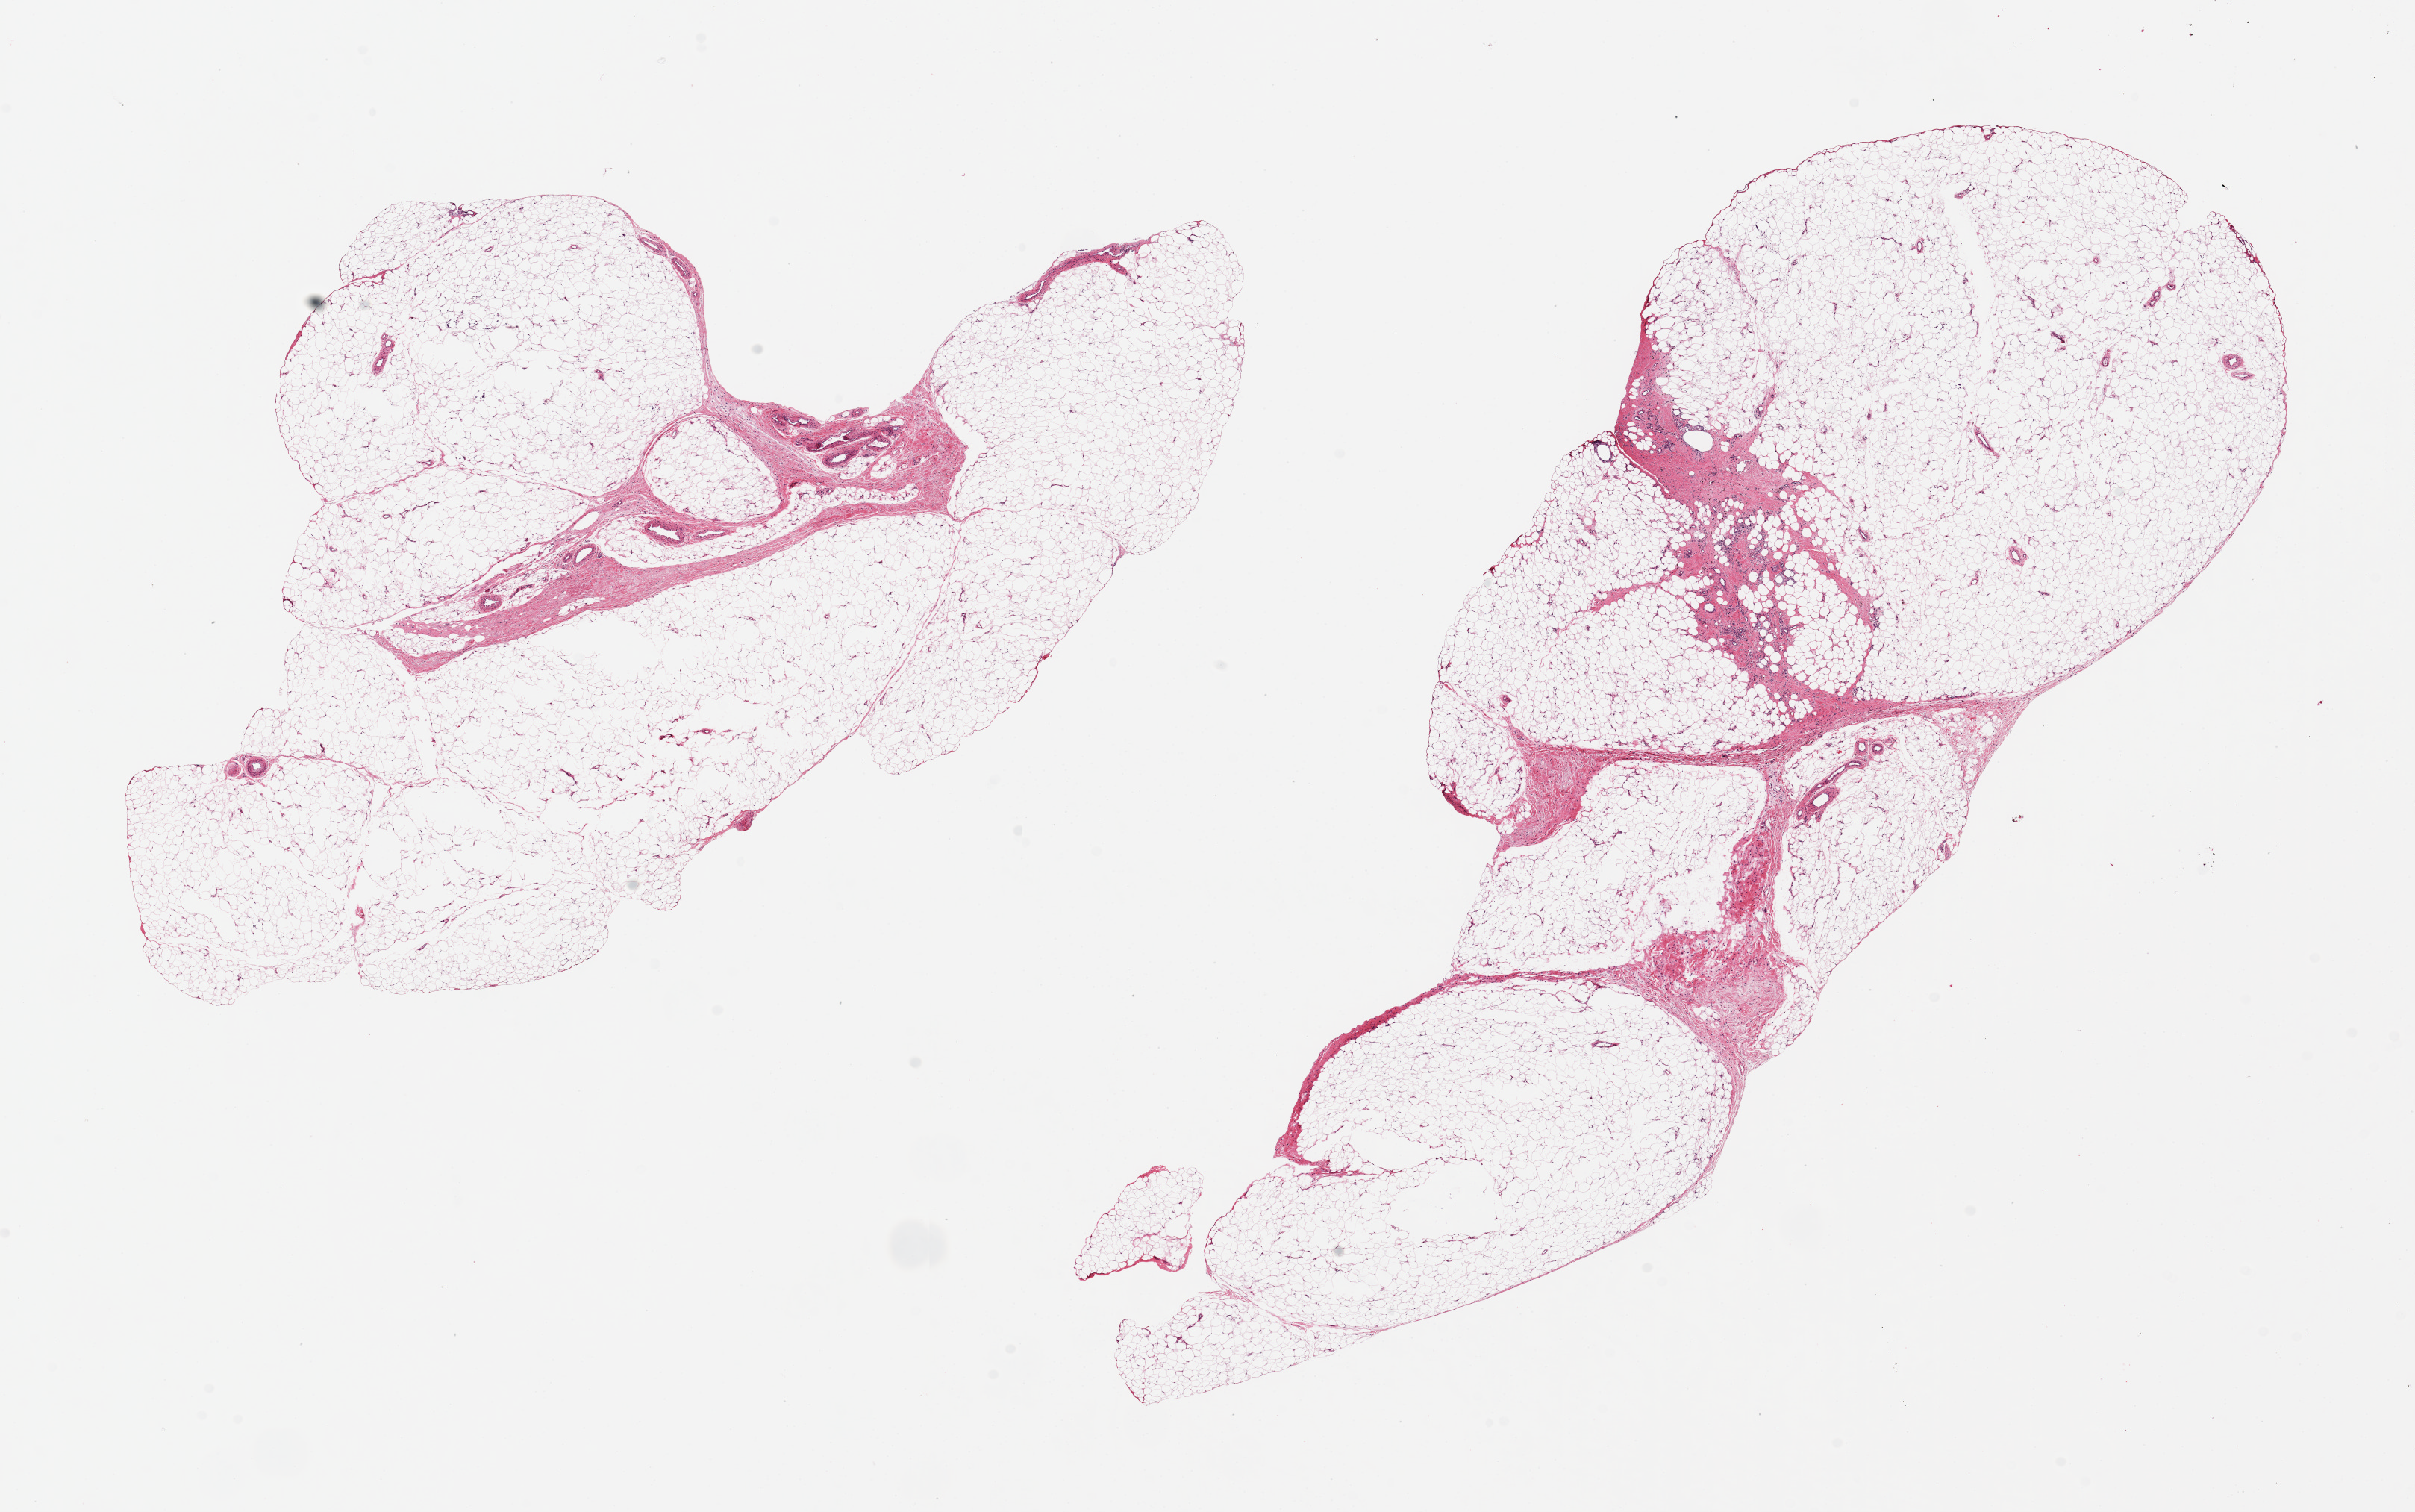
Hematoxylin and eosin (H&E) whole-slide image — shown as a low-resolution overview of the whole scanned area (about 25.6 x 16.0 mm); PAXgene-fixed paraffin-embedded (PFPE) section; sampled site (target tissue): adipose tissue; tissue donor sample. Donor: male.
Pathologist's review note for this sample: 2 pieces ~15x7mm.